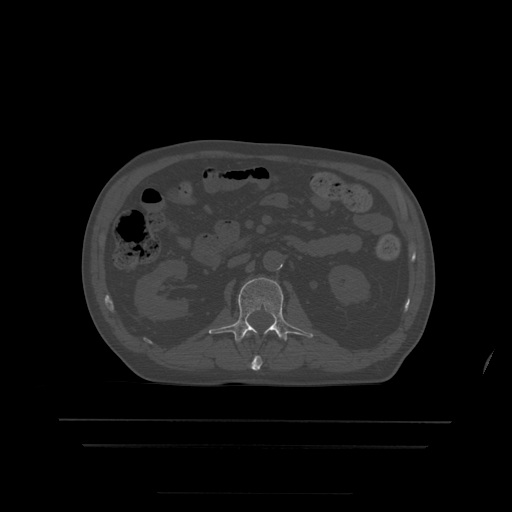
CT including the spine, one axial slice. Position 149 of 522 along the scan axis. Bone window (W 1800 / L 400 HU). 1.25 mm slice thickness. 512 × 512 image matrix, field of view 436 × 436 mm. Patient age 68 years. Case-level facts recorded for this patient, not image findings: primary cancer: urothelial.
Structures marked on this image (semi-automatically segmented with operator editing):
- L1 vertebra: bounding box (x1, y1, x2, y2) in pixels: (244, 333, 263, 371)
- L2 vertebra: (209, 278, 314, 342)